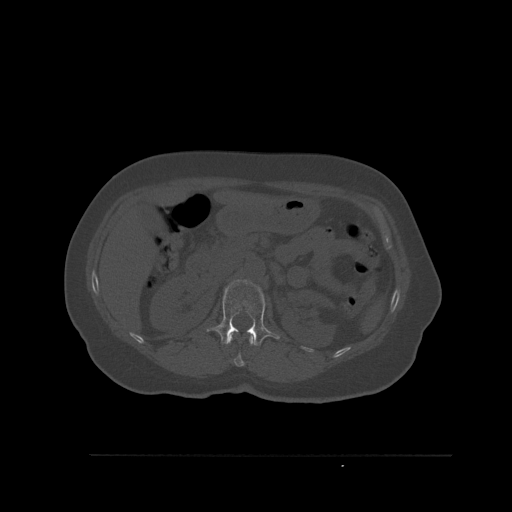
CT including the spine, one axial slice; position 268 of 527 along the scan axis; bone window (W 1800 / L 400 HU); 512 × 512 image matrix. Patient: female, 73 years. From the clinical record (not read from this slice): primary cancer: breast.
Structures marked on this image (semi-automatically segmented with operator editing):
- L1 vertebra: bounding box (x1, y1, x2, y2) in pixels: (206, 279, 280, 346)
- T12 vertebra: (228, 334, 253, 367)